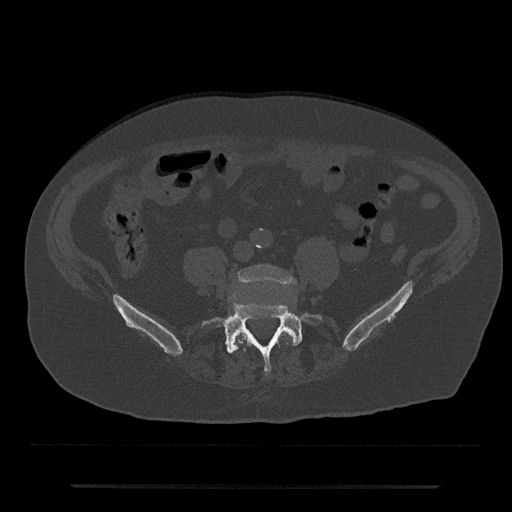
CT including the spine, one axial slice. Position 307 of 797 along the scan axis. 120 kVp. Bone window (W 1800 / L 400 HU). 512 × 512 image matrix, field of view 434 × 434 mm. Male patient, age 80 years. Case-level facts recorded for this patient, not image findings: primary cancer: prostate.
Structures marked on this image (semi-automatic segmentation, software-assisted and operator-edited):
- L4 vertebra: bounding box <235,265,296,345> (left, top, right, bottom; pixels)
- L5 vertebra: <201,301,323,373>